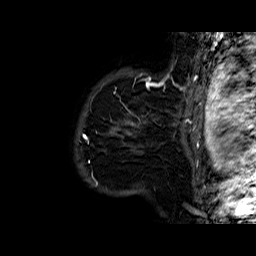
Breast MRI (dynamic contrast-enhanced), one sagittal slice; position 52 of 60 along the scan axis; dynamic contrast-enhanced series, time point 2 of 6 at this slice position (early post-contrast); 1.5 T; TE 6.4 ms, TR 32.8 ms; 4 mm slice thickness; 256 × 256 image matrix, field of view 200 × 200 mm. Female patient. Case-level facts recorded for this patient, not image findings: setting: breast cancer imaged before/during neoadjuvant chemotherapy; receptor status: HR-positive, HER2-negative.
Structures marked on this image (semi-automatic segmentation, software-assisted and operator-edited):
- analysis volume of interest (the breast-tissue region the enhancement analysis was run in; not a lesion): box from (x=86, y=77) to (x=163, y=177) px
- tumour enhancement mask (voxels above the 100 % enhancement threshold inside the analysis volume of interest): (x=131, y=81)–(x=163, y=125)